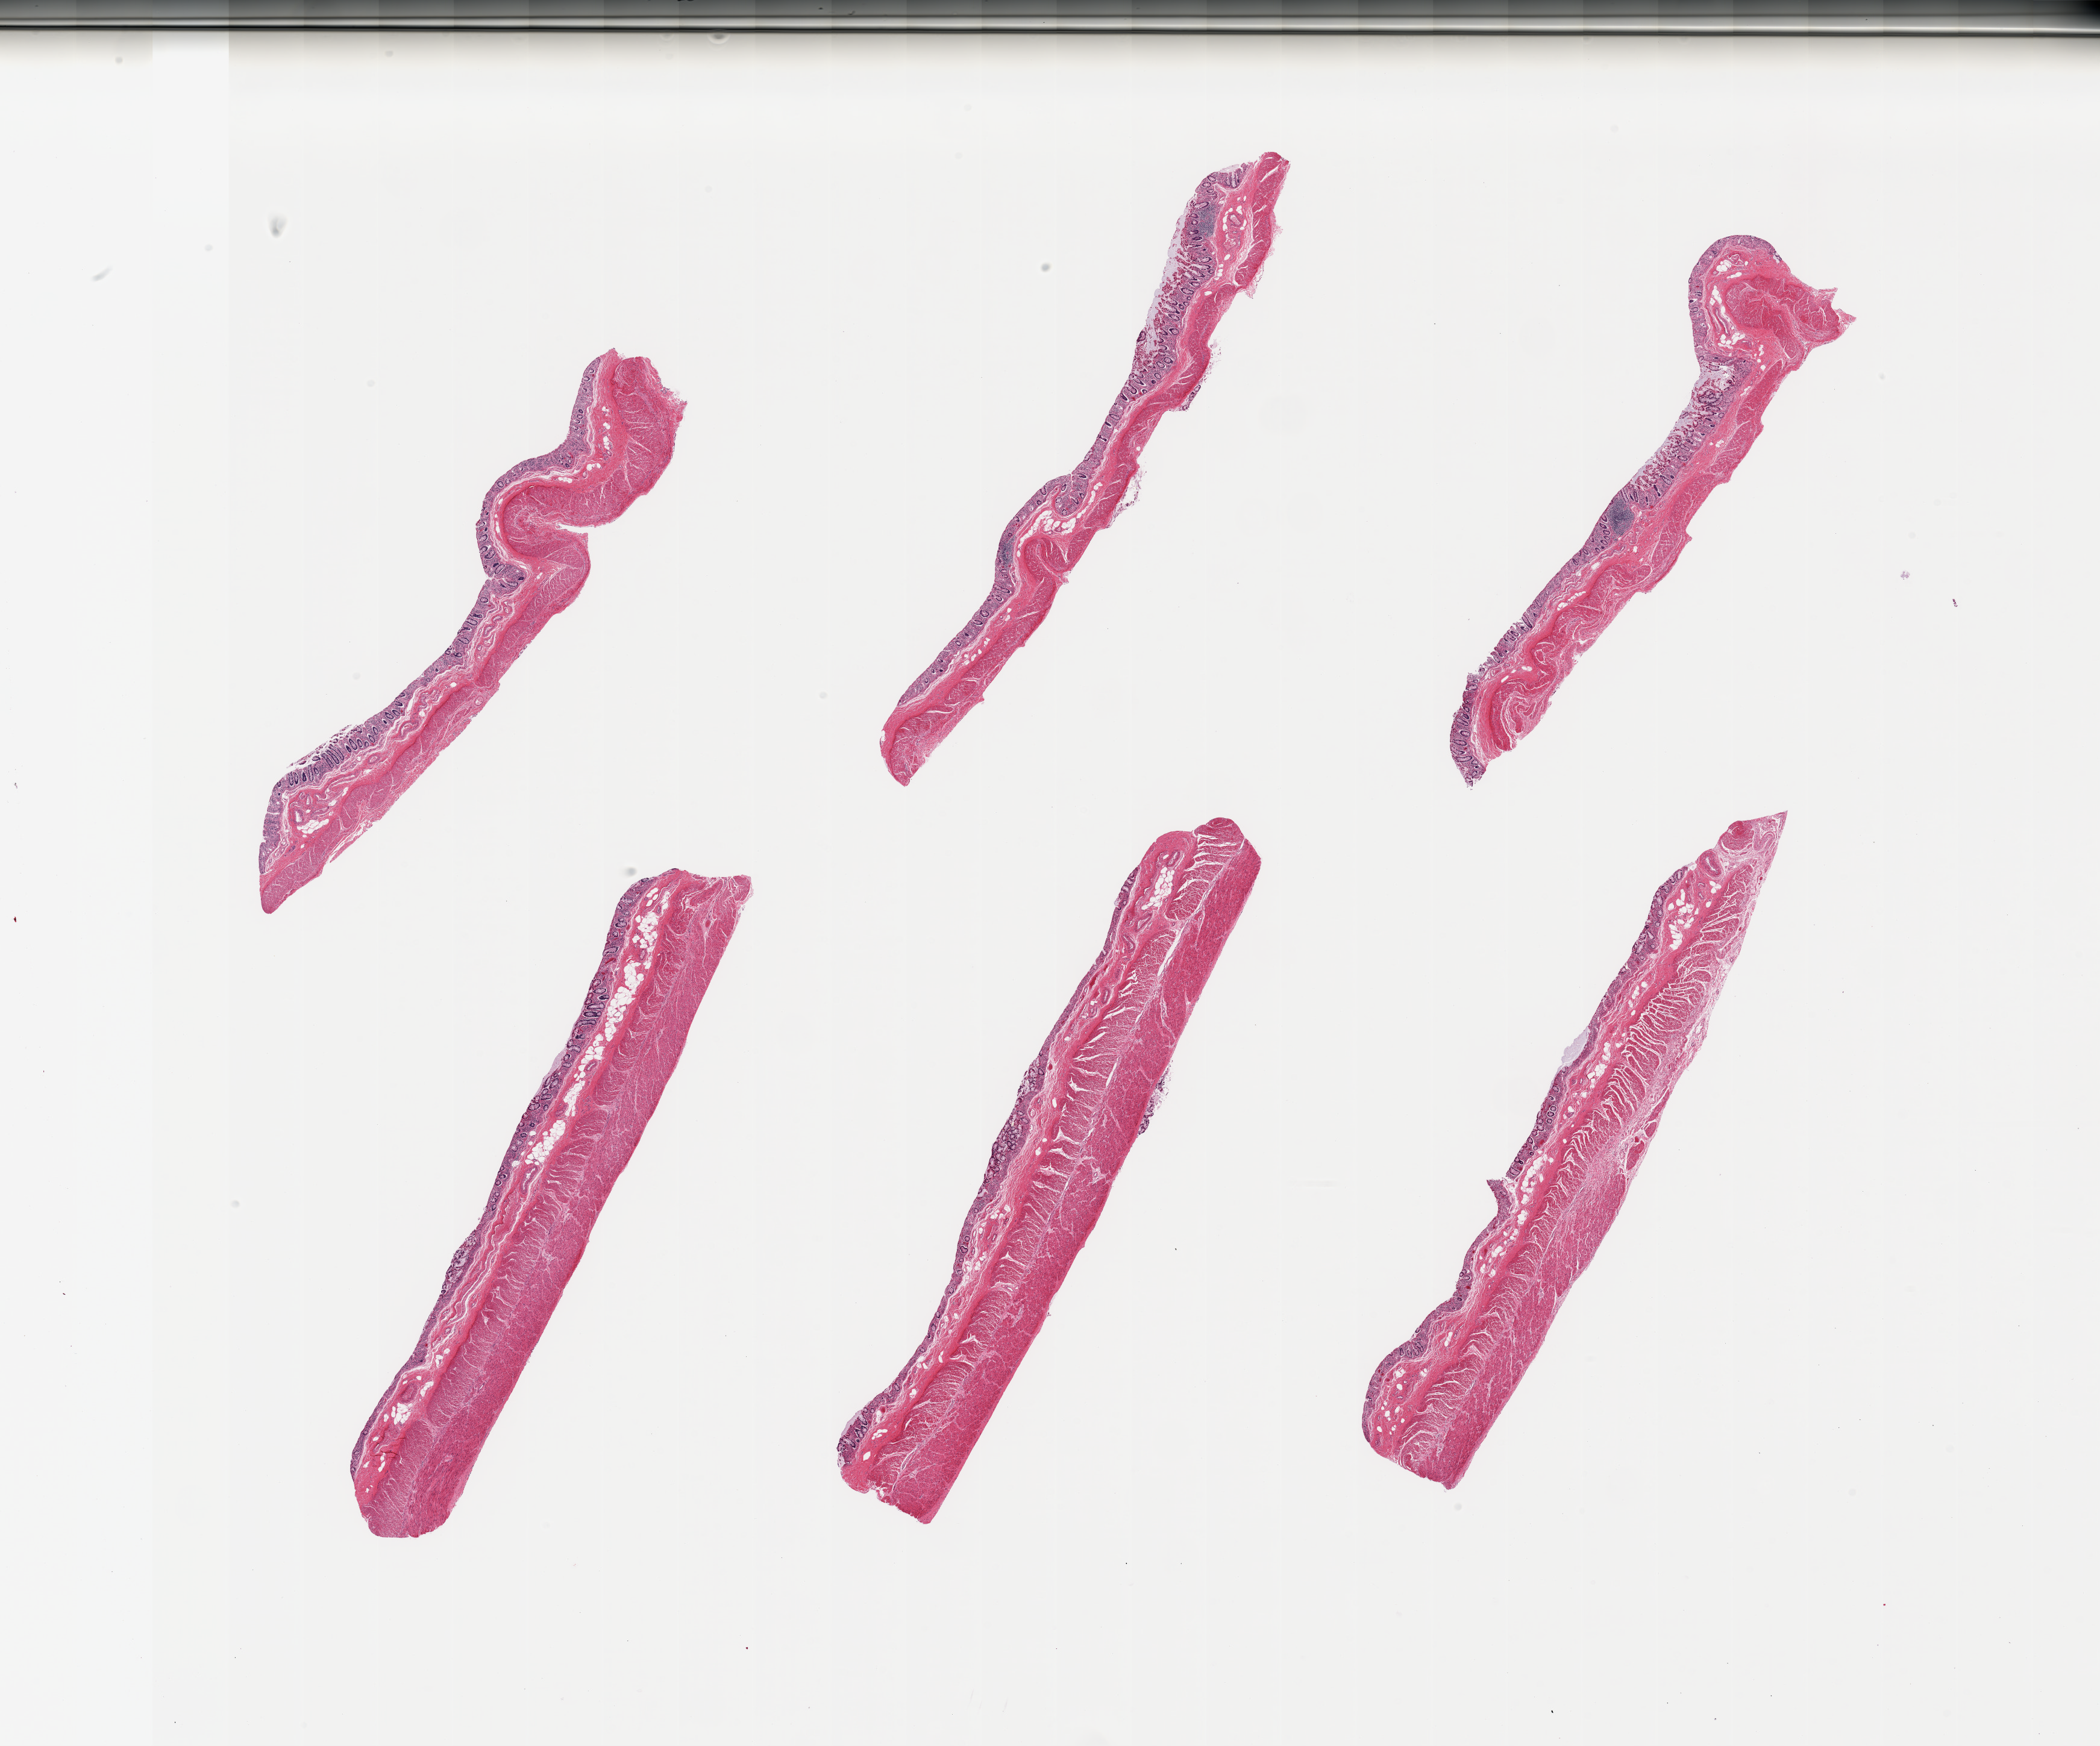
Digitized haematoxylin and eosin-stained section, brightfield, shown as a low-resolution overview of the whole scanned area (about 27.6 x 22.9 mm), PAXgene-fixed, paraffin-embedded tissue, section of transverse colon (target tissue), donor tissue sample.
* pathologist's review note for this sample: 6 pieces; mucosa partly autolyzed. muscle intact; well dissected